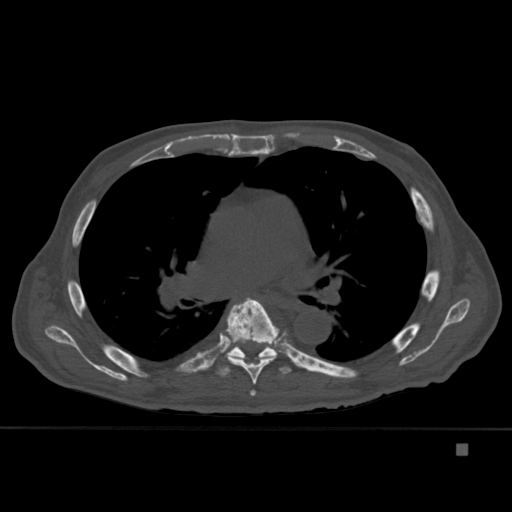
CT including the spine, one axial slice; position 289 of 451 along the scan axis; bone window (W 1800 / L 400 HU); 1.5 mm slice thickness; 512 × 512 image matrix, field of view 378 × 378 mm. Male patient, age 75 years. From the clinical record (not read from this slice): primary cancer: prostate.
Outlined on this slice (semi-automatically segmented with operator editing):
- T5 vertebra: bounding box <250,390,256,396> (left, top, right, bottom; pixels)
- T6 vertebra: <223,297,279,385>
- T7 vertebra: <206,343,296,377>